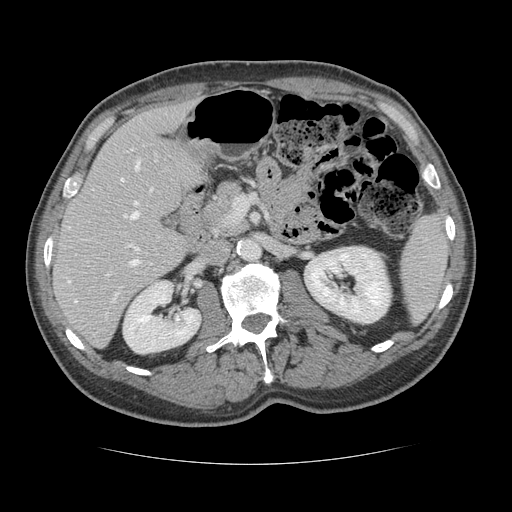
Contrast-enhanced abdominal CT, one axial slice. Position 67 of 134 along the scan axis. Reconstruction kernel STANDARD. 120 kVp. Intravenous contrast given. Soft-tissue window (W 400 / L 40 HU). 2.5 mm slice thickness. 512 × 512 image matrix, field of view 377 × 377 mm. Male patient, age 68 years. From the clinical record (not read from this slice): diagnosis: colorectal cancer liver metastases, imaged before liver resection; multiple liver metastases: yes; largest metastasis: 2.2 cm; disease in both lobes: no.
Annotated regions visible in this slice (outlined manually by an expert reader):
- hepatic veins: bounding box [x1, y1, x2, y2] px = [68, 160, 153, 302]
- liver: [54, 104, 206, 346]
- planned liver remnant (the part of the liver to remain after resection): [54, 104, 206, 336]
- portal vein (with intrahepatic branches): [124, 214, 139, 266]